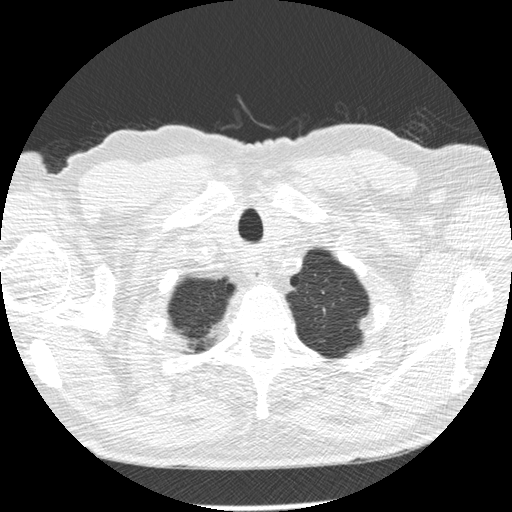
Chest CT (low-dose screening protocol), one axial image; second annual screen; lung window (W 1500 / L -600 HU); slice 21 of 276 in the series. Male participant, aged 73 years at enrolment.
Expert-annotated lung lesion, box from (x=346, y=306) to (x=386, y=346) px. No non-calcified nodule or mass ≥4 mm was recorded by the screening reader at this exam. Official screen result: negative screen, minor abnormalities not suspicious for lung cancer. Later outcome: lung cancer diagnosed 457 days after this screen — adenocarcinoma, NOS, left upper lobe, poorly differentiated (G3), stage IB (AJCC 6th edition), 10 mm at pathology.